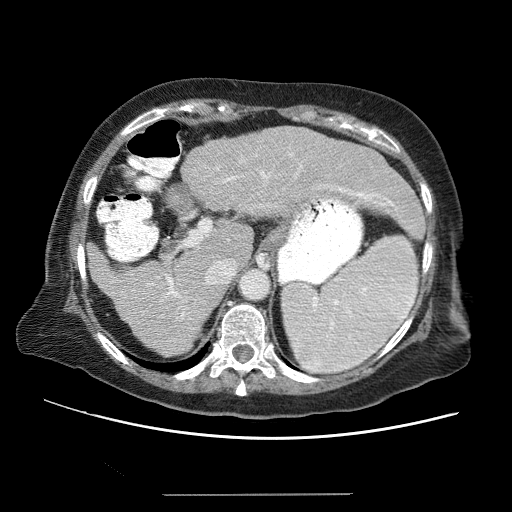
Contrast-enhanced abdominal CT (liver protocol), one axial slice; slice 40 of 65 in the series (ordered by position); 120 kVp; soft-tissue window (W 400 / L 40 HU); 2.5 mm slice thickness; 512 × 512 image matrix. From the clinical record (not read from this slice): diagnosis: hepatocellular carcinoma (patient treated with transarterial chemoembolisation; whether this scan precedes or follows treatment is not stated here); TNM stage (as recorded): Stage-IIIB; Child-Pugh class: A.
Annotated regions visible in this slice (semi-automatic segmentation, software-assisted and operator-edited):
- liver parenchyma outside the tumour (the mass and vessels are separate outlines, so this box may not span the whole liver): bounding box [x1, y1, x2, y2] px = [86, 126, 416, 354]
- liver vessels: [117, 142, 403, 338]